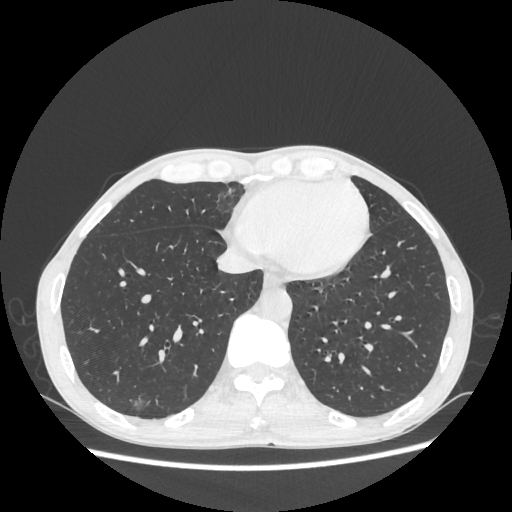
Chest CT, one axial slice; slice 81 of 270 in the series (ordered by position); reconstruction kernel STANDARD; 100 kVp; lung window (W 1500 / L -600 HU); 1.25 mm slice thickness; 512 × 512 image matrix, field of view 360 × 360 mm. Male patient, age 60 years. From the clinical record (not read from this slice): clinical TNM (as recorded): T1c N0 M0; histopathological grade: G2.
Annotated regions visible in this slice (rectangle marked by the reading radiologist):
- lung tumour (recorded histology: adenocarcinoma): bounding box (x1, y1, x2, y2) in pixels: (125, 389, 155, 418)